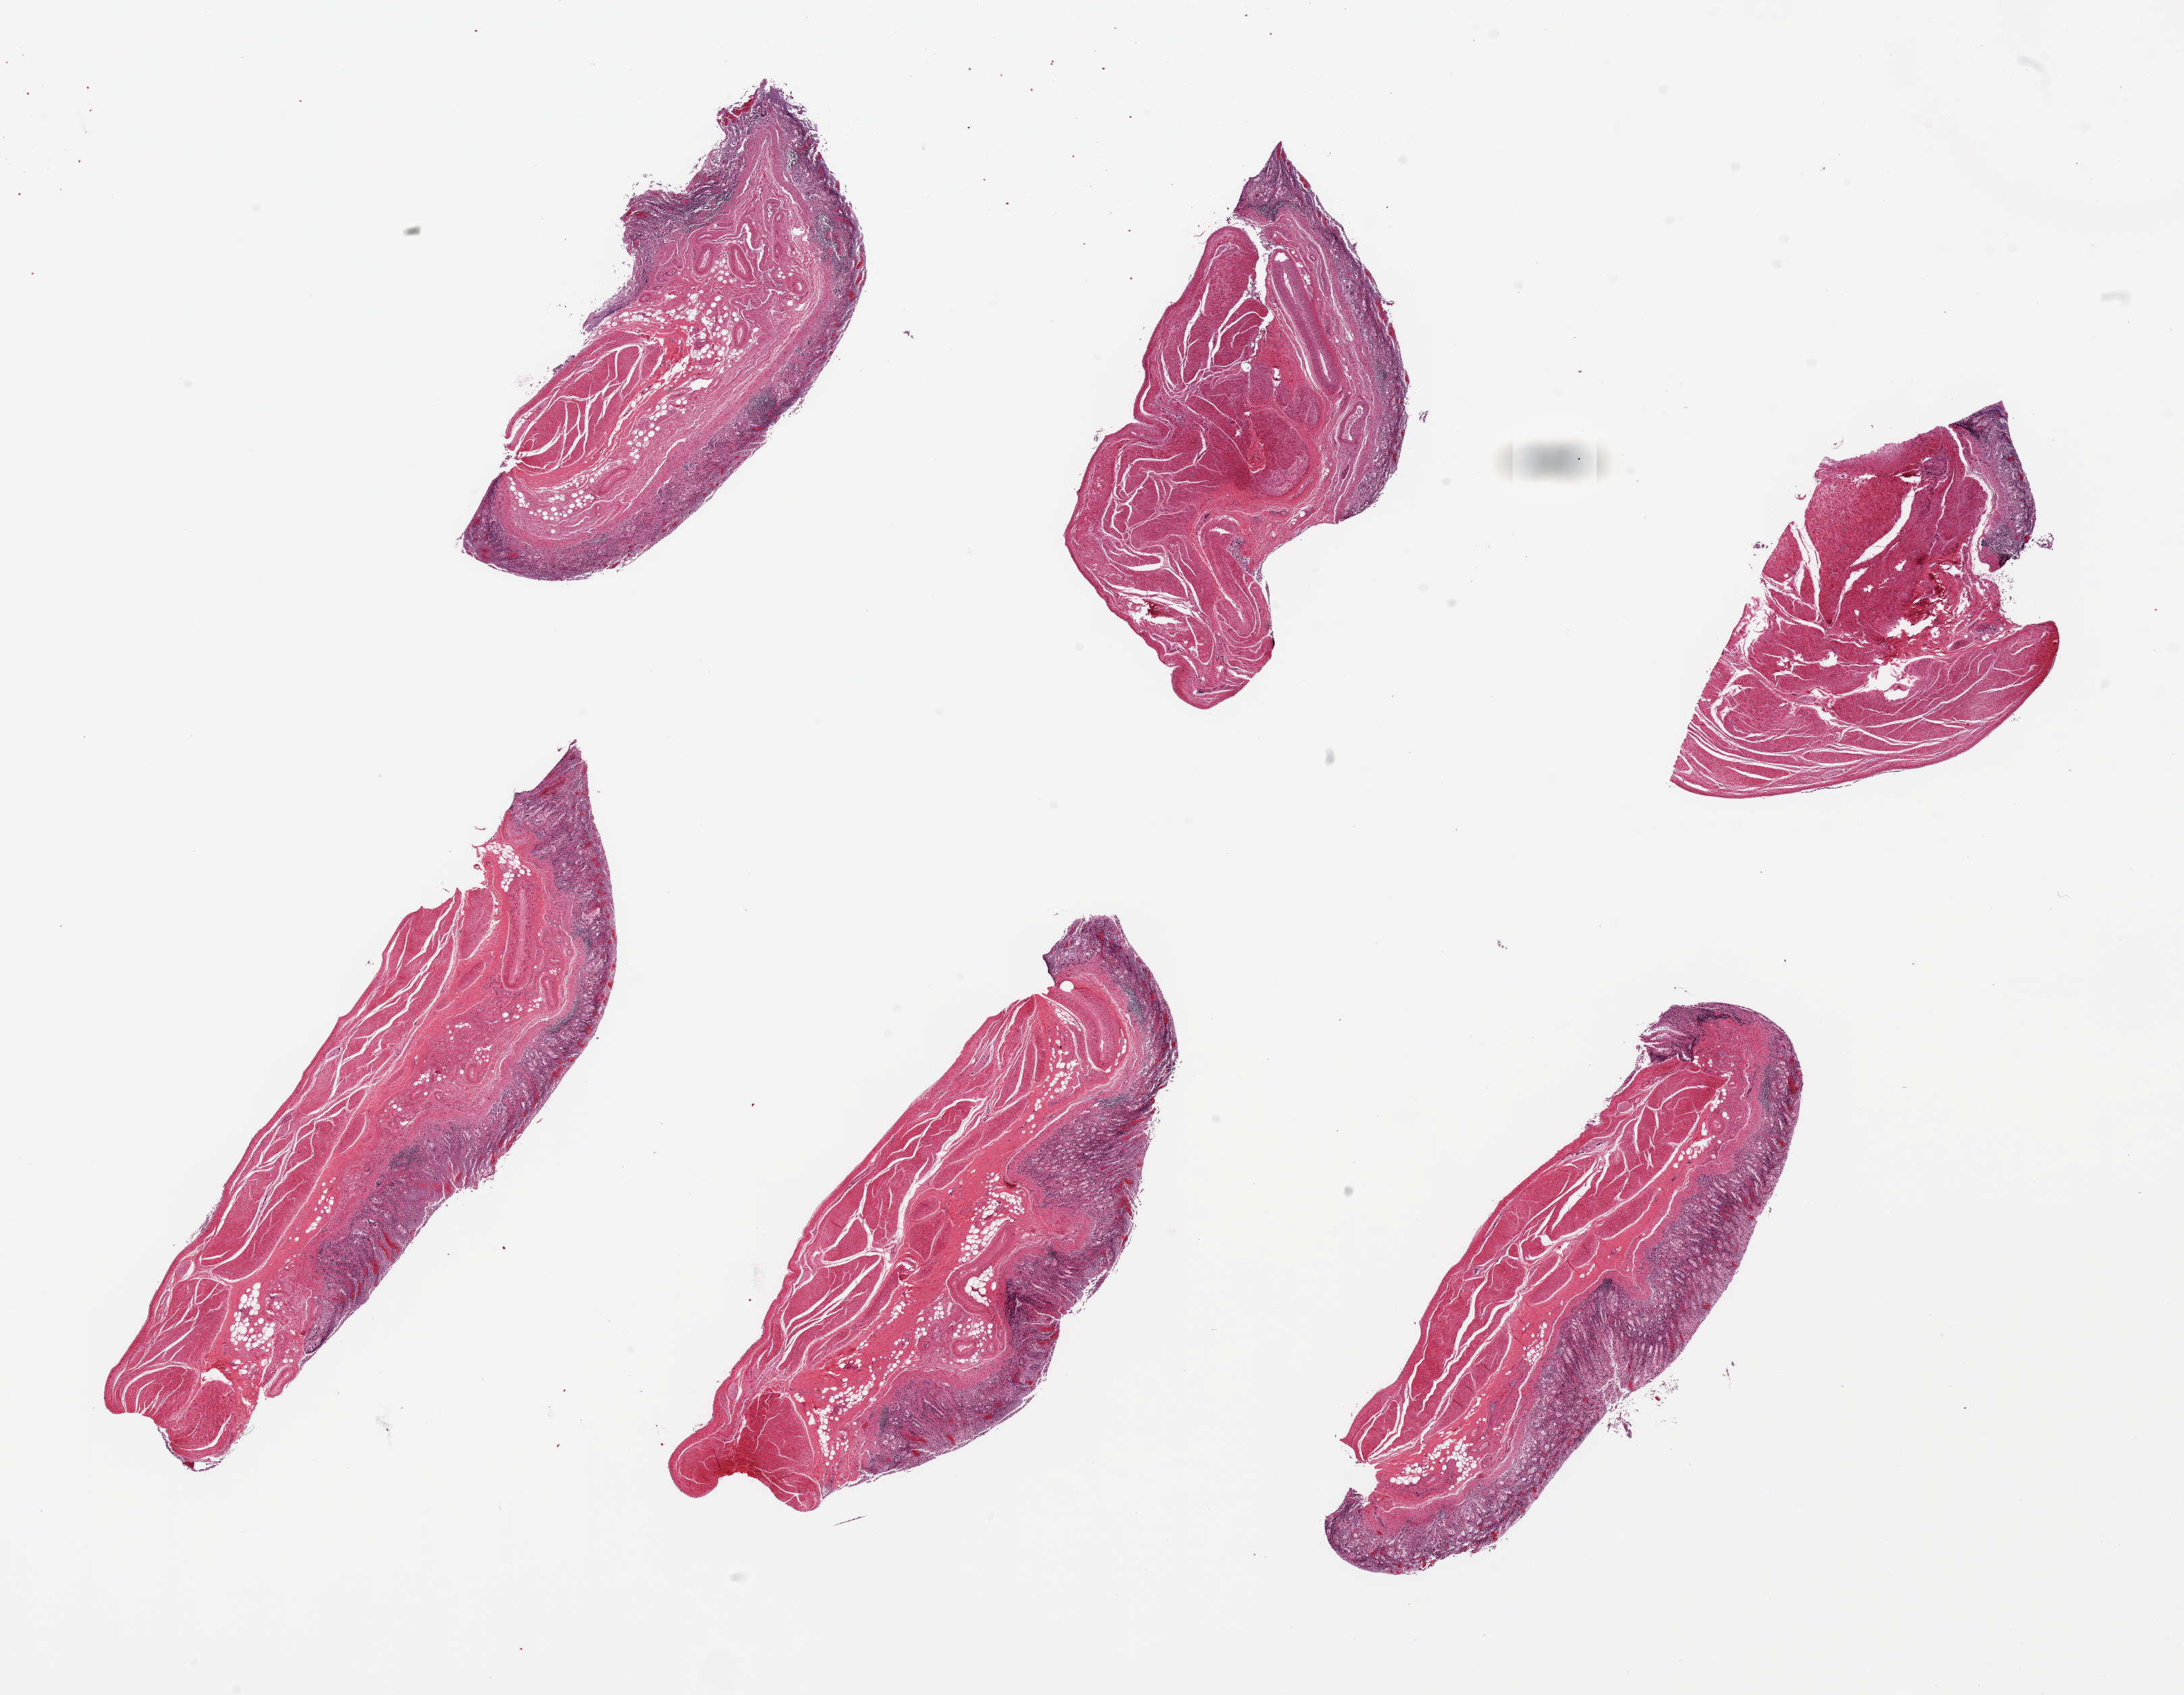
Whole-slide image, H&E stain, whole scanned area (about 25.6 x 19.9 mm) shown as a low-resolution overview; PAXgene-fixed paraffin-embedded (PFPE) section; target tissue: stomach; tissue donor sample. Donor sex: male.
* reviewer comment on this tissue sample: 6 pieces up to 8x2.5 mm; glands completely autolyzed